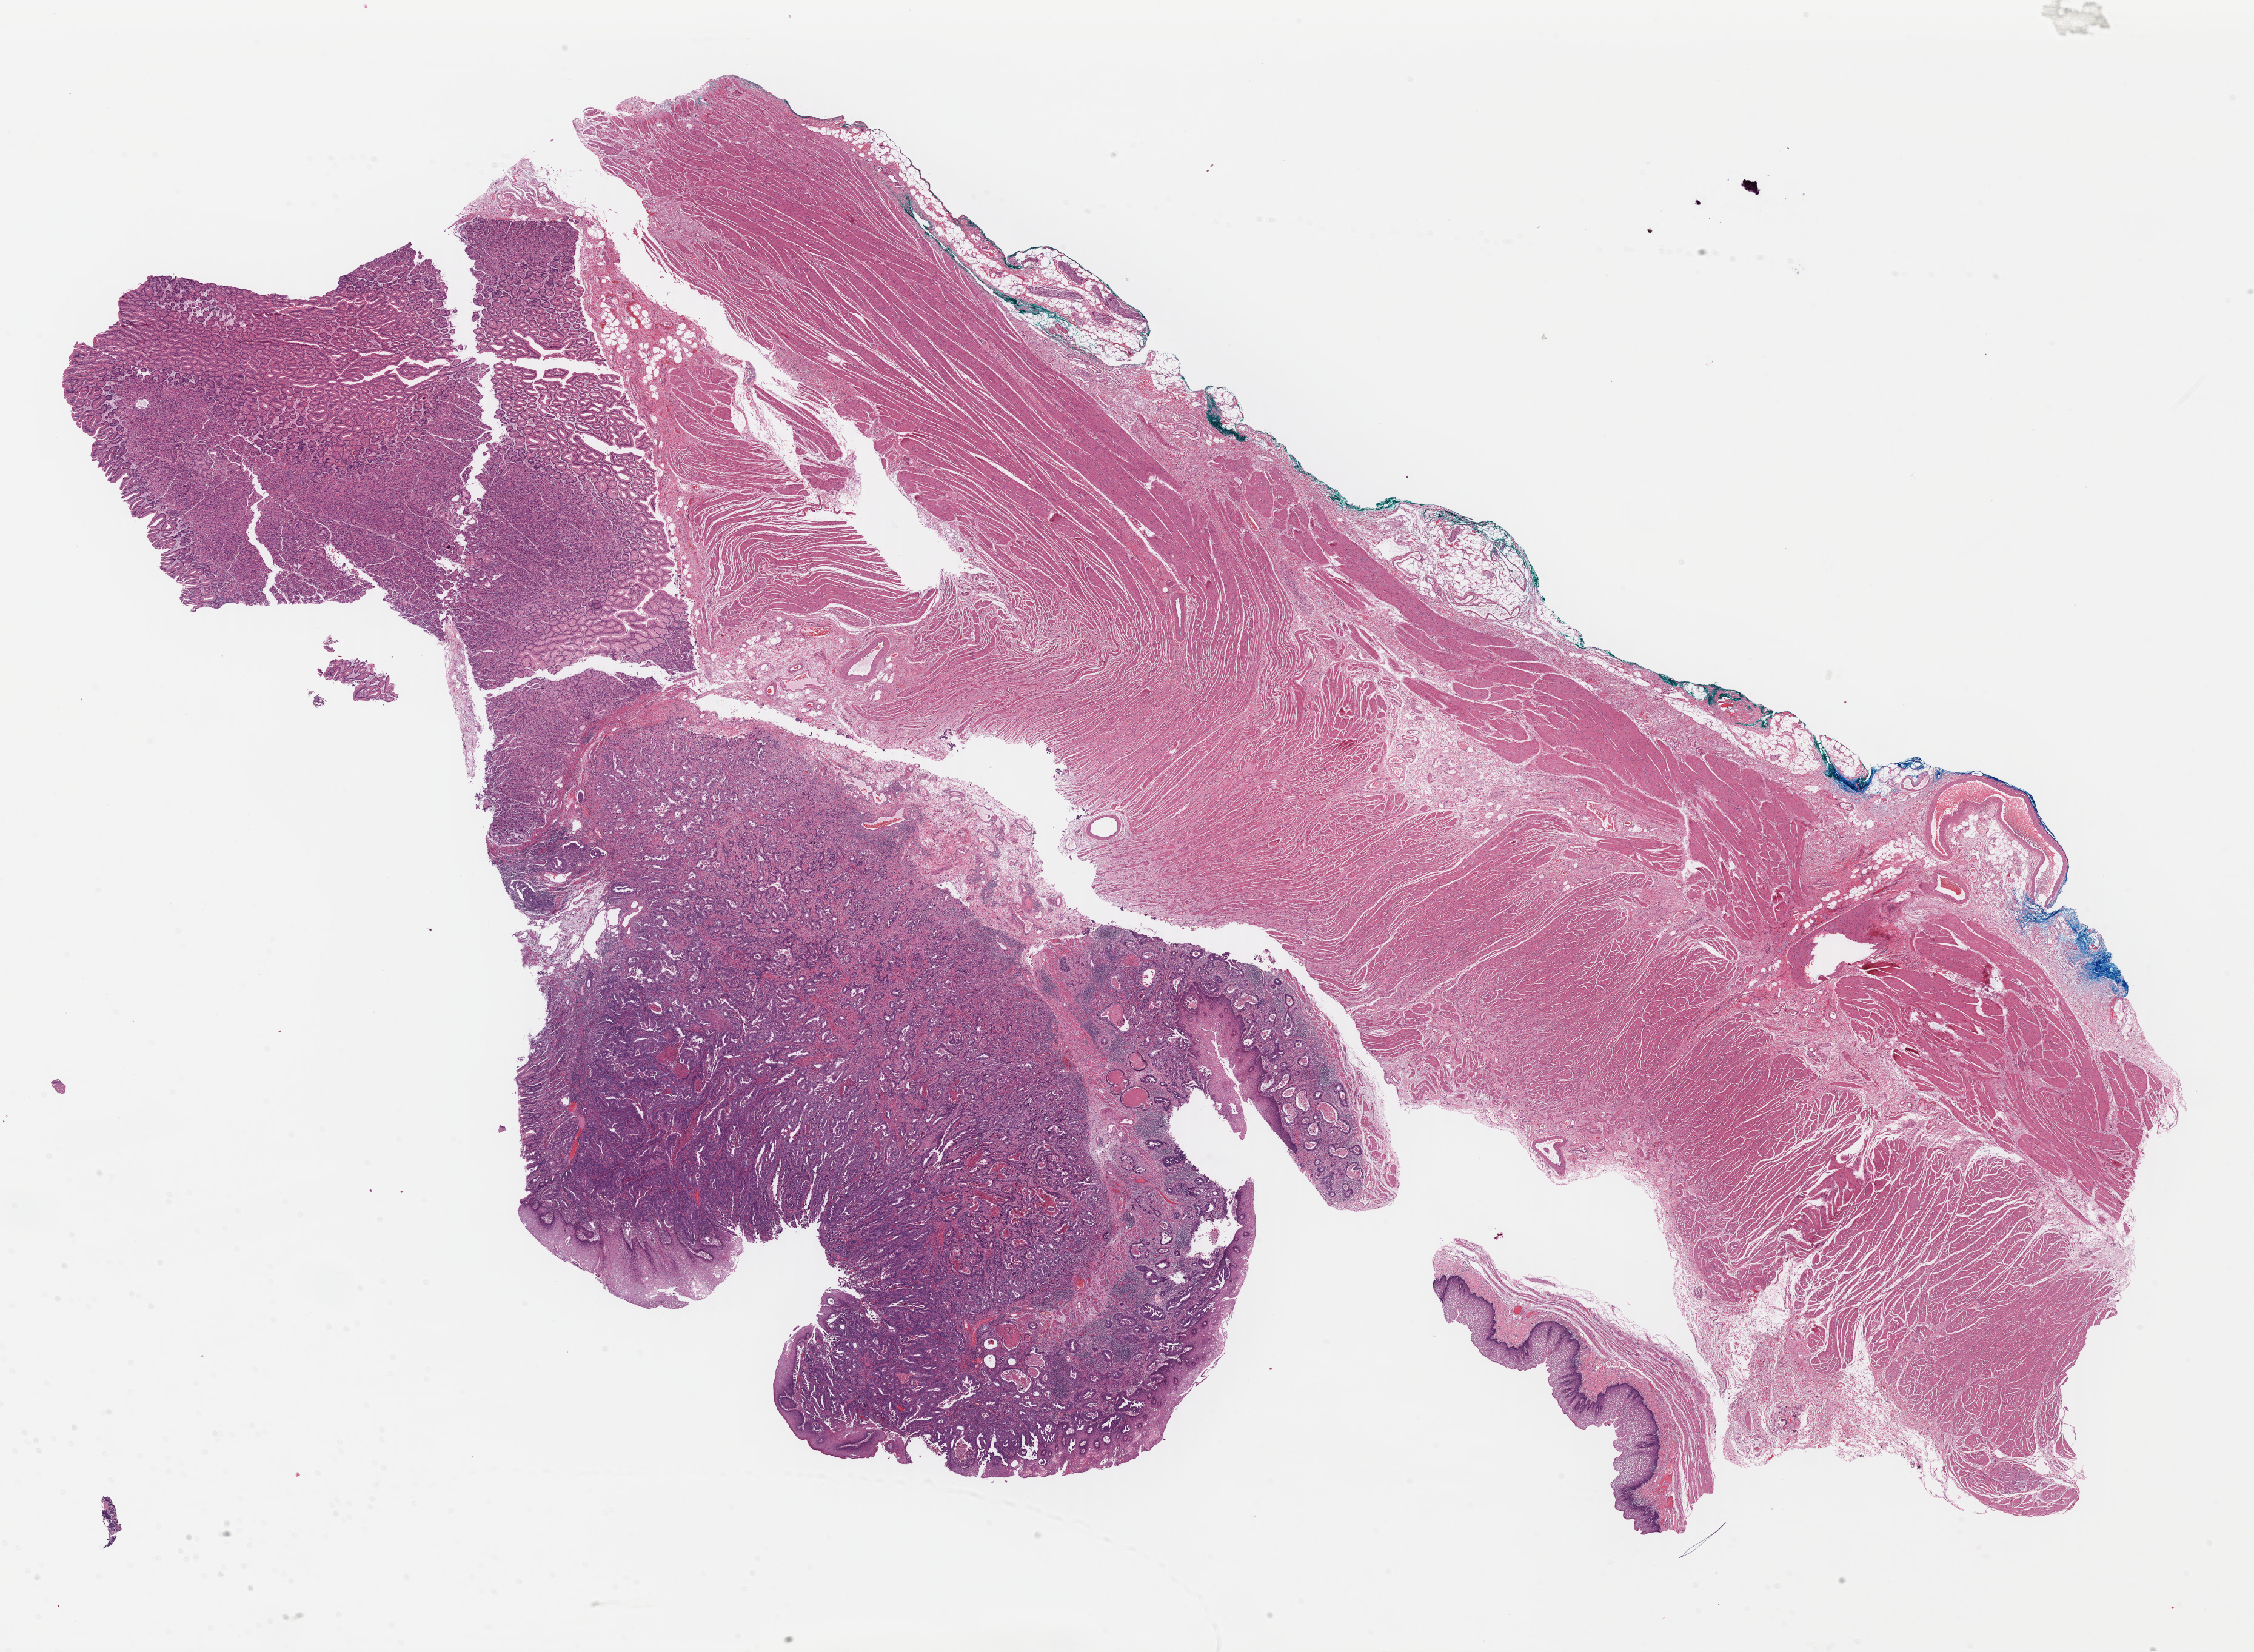
Whole-slide histology image, Hematoxylin and eosin (H&E) stained, low-resolution overview of the scanned area, about 29.2 x 21.4 mm; formalin-fixed paraffin-embedded (FFPE) diagnostic section; sample: primary tumour, esophagus. Patient: male, age at initial diagnosis 71 years. Histologic grade: GX (grade cannot be assessed).
TNM: T1 N0 M0. Diagnosis: Adenocarcinoma, NOS (lower third of esophagus). AJCC pathologic stage: I (7th edition). Lymph nodes positive (case pathology): 0 of 9 examined.